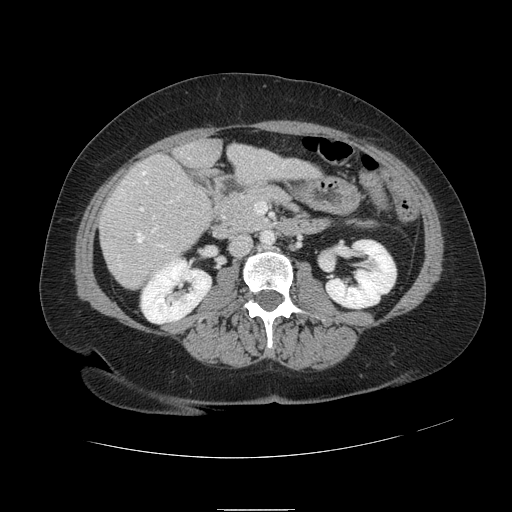
Contrast-enhanced abdominal CT, one axial slice; slice 33 of 121 in the series (ordered by position); 120 kVp; intravenous contrast given; soft-tissue window (W 400 / L 40 HU); 2.5 mm slice thickness; 512 × 512 image matrix, field of view 400 × 400 mm. Female patient, age 52 years. From the clinical record (not read from this slice): diagnosis: colorectal cancer liver metastases, imaged before liver resection; multiple liver metastases: yes; largest metastasis: 6.3 cm; chemotherapy before resection: yes.
Structures marked on this image (outlined manually by an expert reader):
- hepatic veins: bounding box (x1, y1, x2, y2) in pixels: (119, 172, 172, 267)
- liver: (100, 141, 316, 289)
- planned liver remnant (the part of the liver to remain after resection): (175, 141, 315, 180)
- portal vein (with intrahepatic branches): (140, 208, 144, 211)